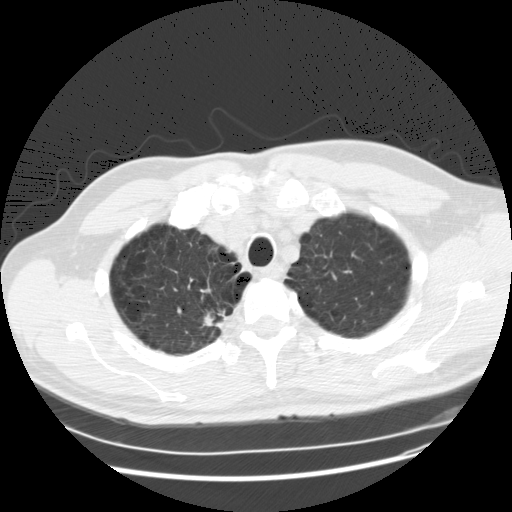
Axial slice from a low-dose chest CT screening exam. Baseline screening round. Lung window (W 1500 / L -600 HU). Standard (soft-tissue) reconstruction kernel (STANDARD). 120 kVp. Slice 22 of 132 in the series. 512 × 512 image matrix, field of view 380 × 380 mm. Male, age 61 years at enrolment.
- Expert-annotated lung lesion, box from (x=195, y=291) to (x=235, y=341) px.
- The exam's reader record, not a measurement of the box and not confirmed to be the same lesion: non-calcified nodule or mass ≥4 mm, right upper lobe, 19 × 13 mm, poorly defined margins, soft tissue attenuation.
- Official screen result: positive, change unspecified: nodule(s) >= 4 mm or enlarging nodule(s), mass(es), or other non-specific abnormalities suspicious for lung cancer.
- Later outcome: lung cancer diagnosed 62 days after this screen — squamous cell carcinoma, NOS, right upper lobe, poorly differentiated (G3), stage IA (AJCC 6th edition), 20 mm at pathology.